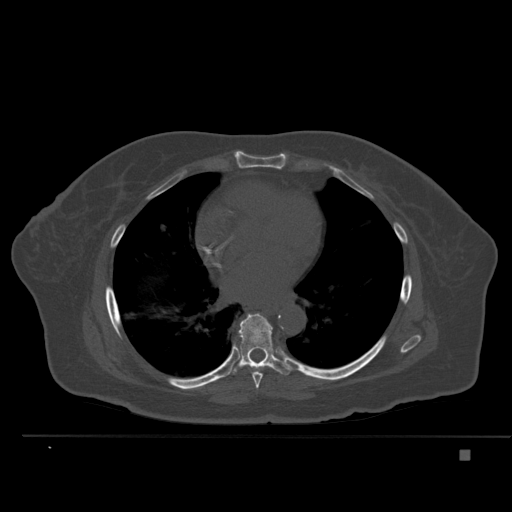
CT including the spine, one axial slice. Slice 316 of 477 in the series (ordered by position). Bone window (W 1800 / L 400 HU). 1.5 mm slice thickness. 512 × 512 image matrix. Female patient, age 74 years. From the clinical record (not read from this slice): primary cancer: colon.
Outlined on this slice (semi-automatically segmented with operator editing):
- T7 vertebra: bounding box <252,372,263,389> (left, top, right, bottom; pixels)
- T8 vertebra: <228,313,289,376>